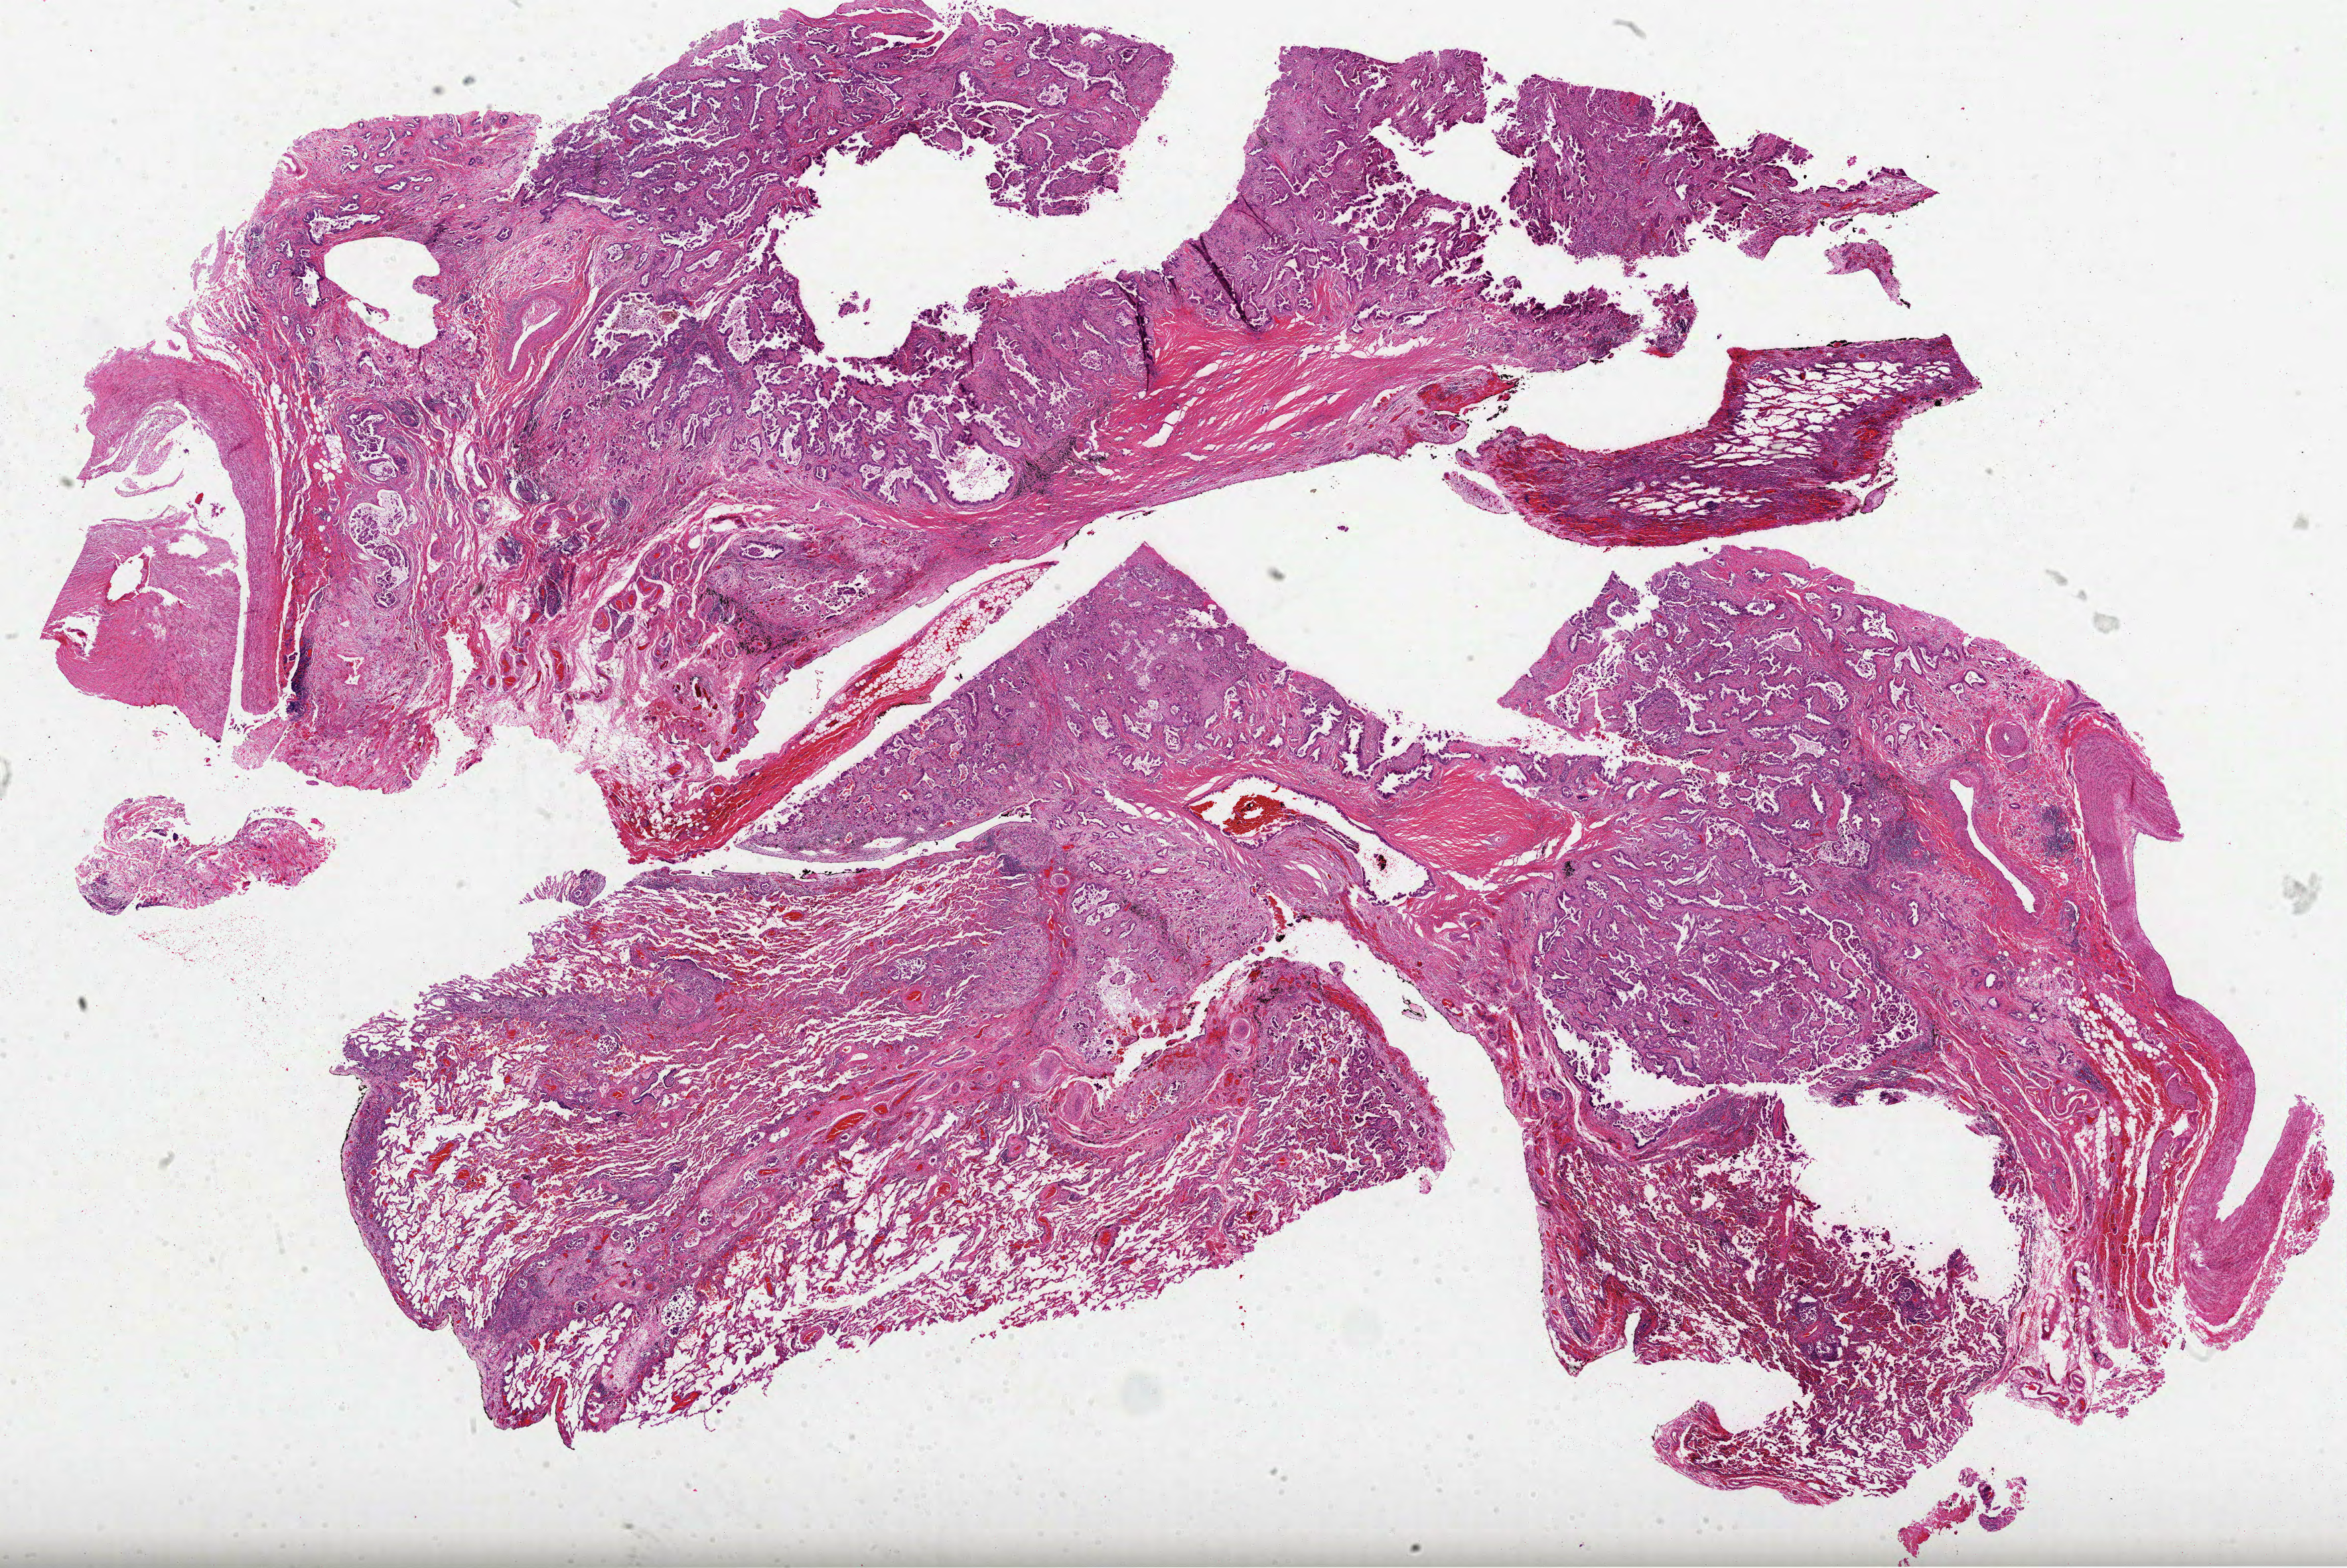
Whole-slide histology image, H&E — whole scanned area (about 28.5 x 19.1 mm, acquisition: 40x scan) shown as a low-resolution overview, FFPE section, lung, primary tumour sample. Female patient; age at initial diagnosis 45 years.
AJCC pathologic stage: IIIA (4th edition). Diagnosis: Adenocarcinoma, NOS (upper lobe, lung). Laterality: left. TNM: T3 N2 M0.